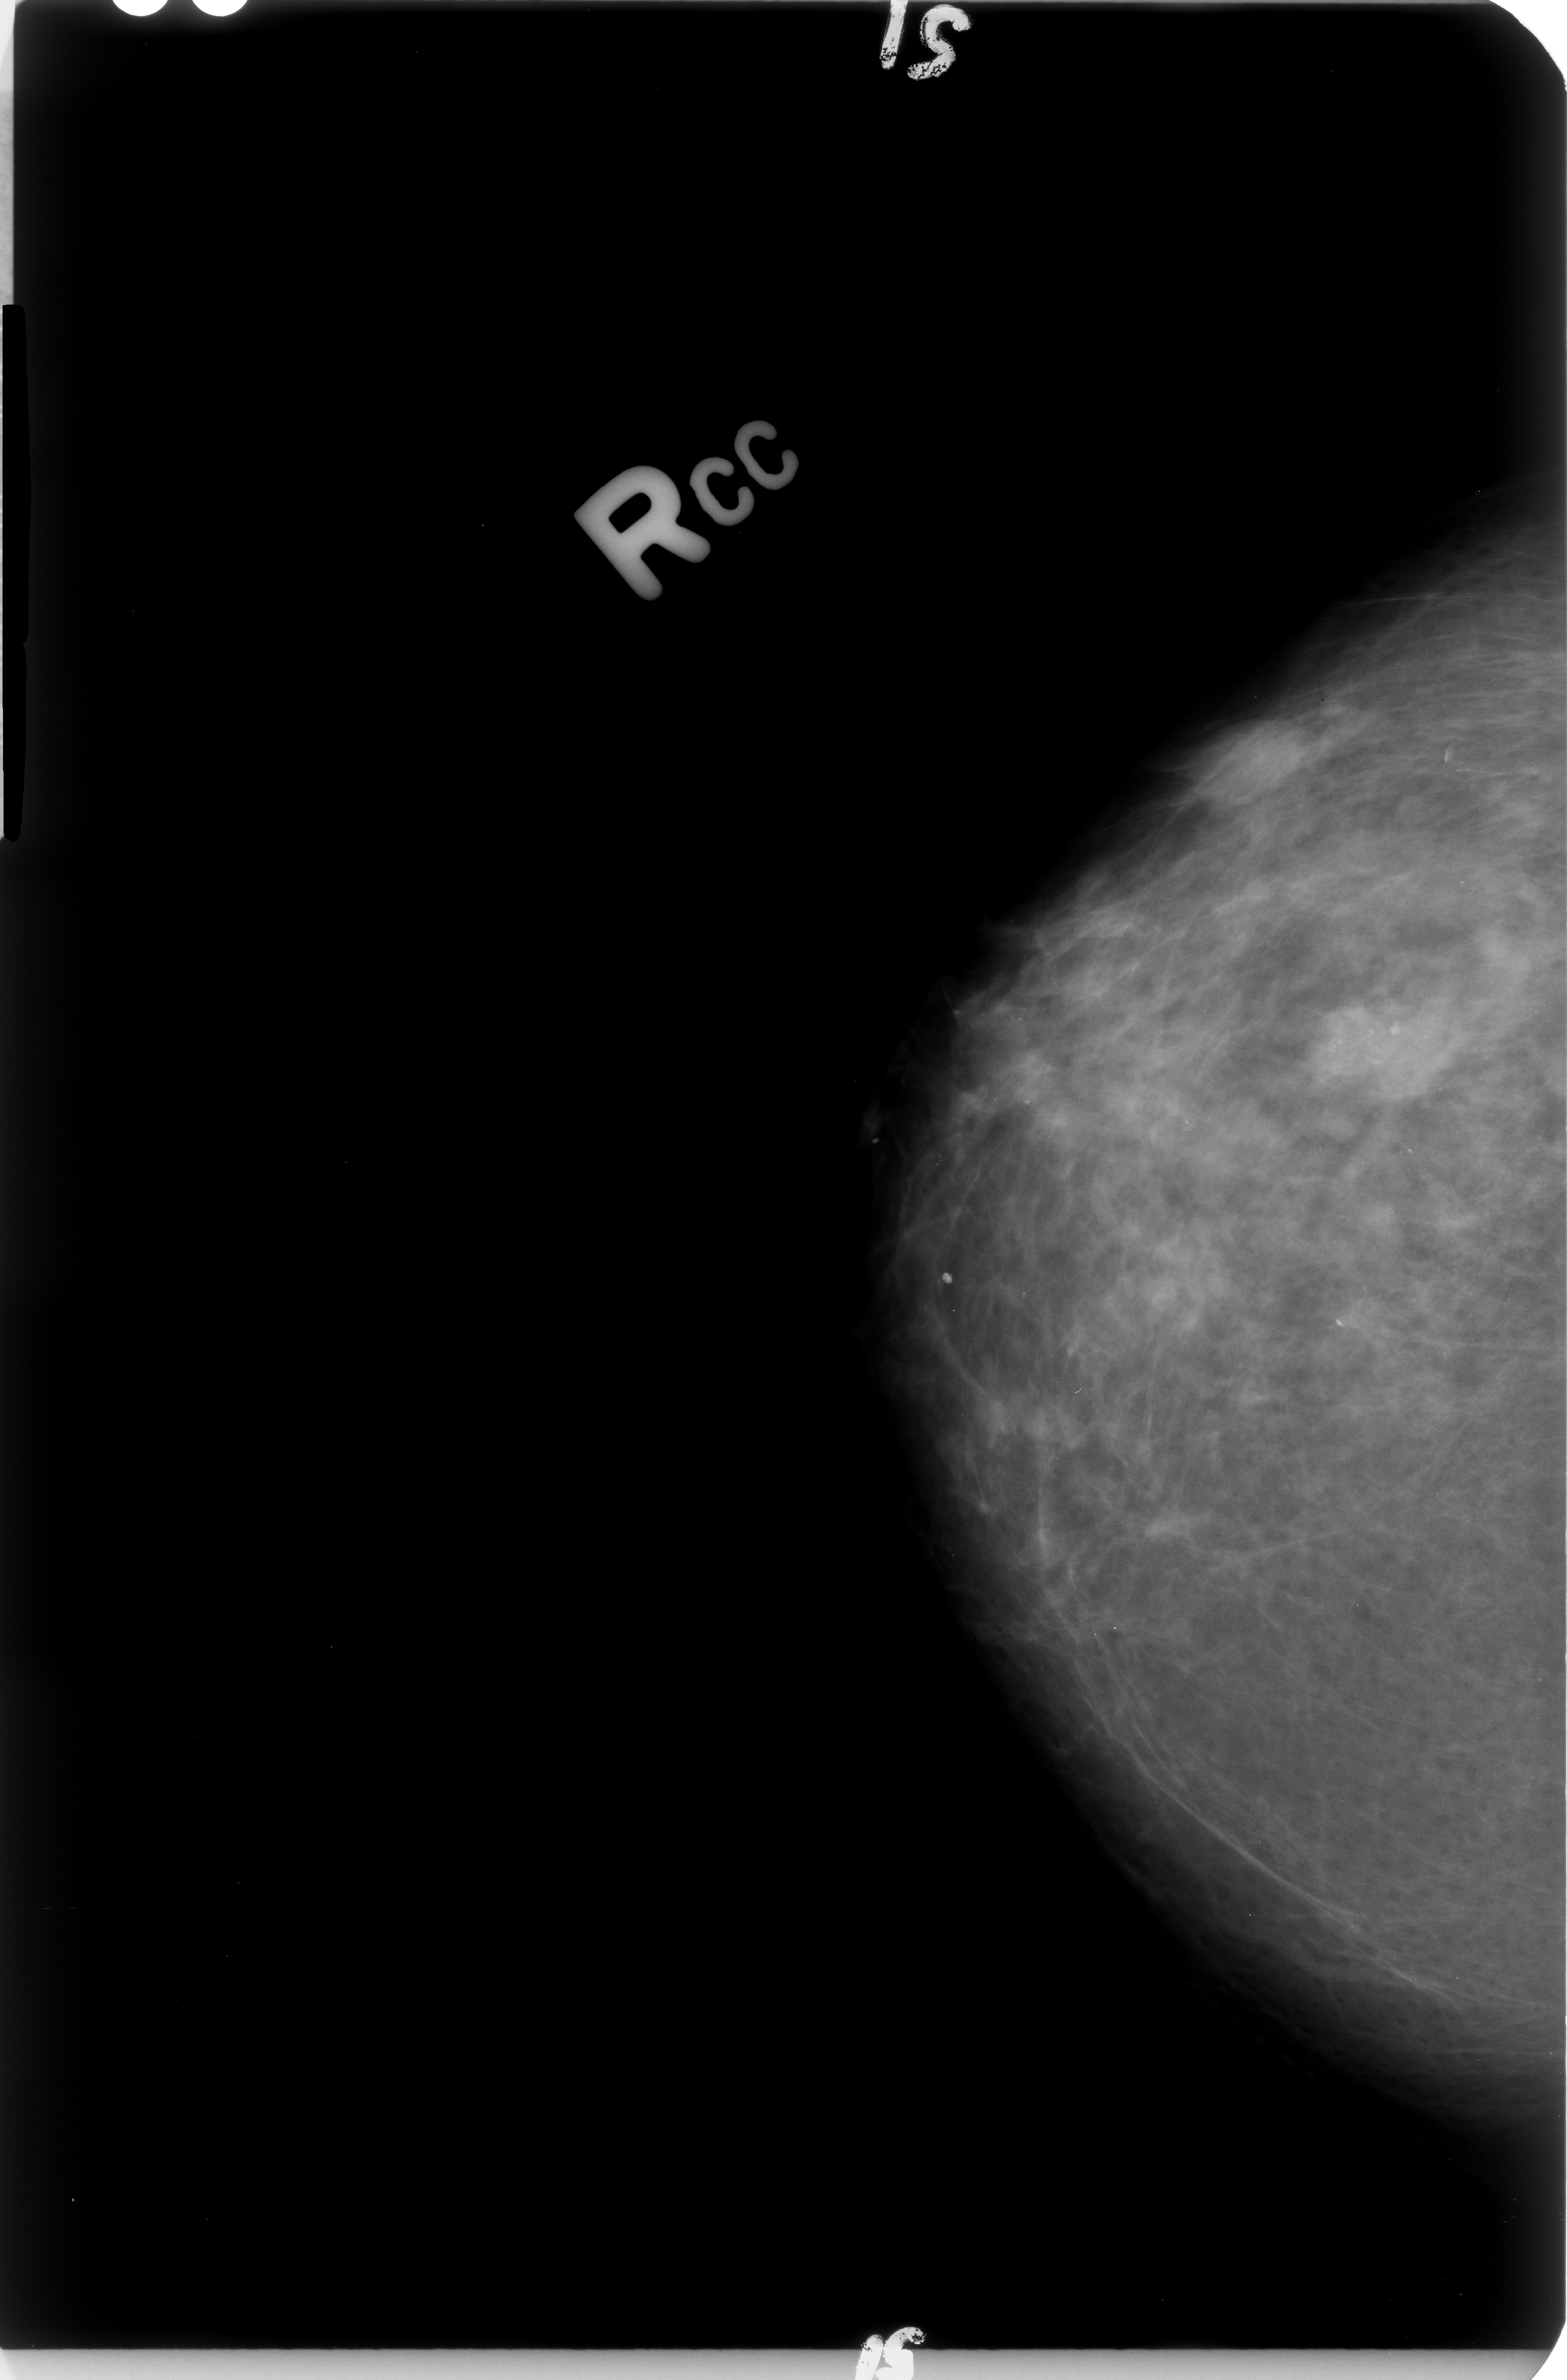
Mammogram (digitized film); right breast; CC view; breast composition: scattered fibroglandular densities (BI-RADS density category 2 of 4); 1567 × 2380 image matrix.
Marked abnormalities (boxes around the expert regions of interest):
- mass; BI-RADS assessment category 0 (incomplete: needs additional imaging); pathology result (as recorded, not read from the image): benign: bounding box (x1, y1, x2, y2) in pixels: (1186, 717, 1310, 792)